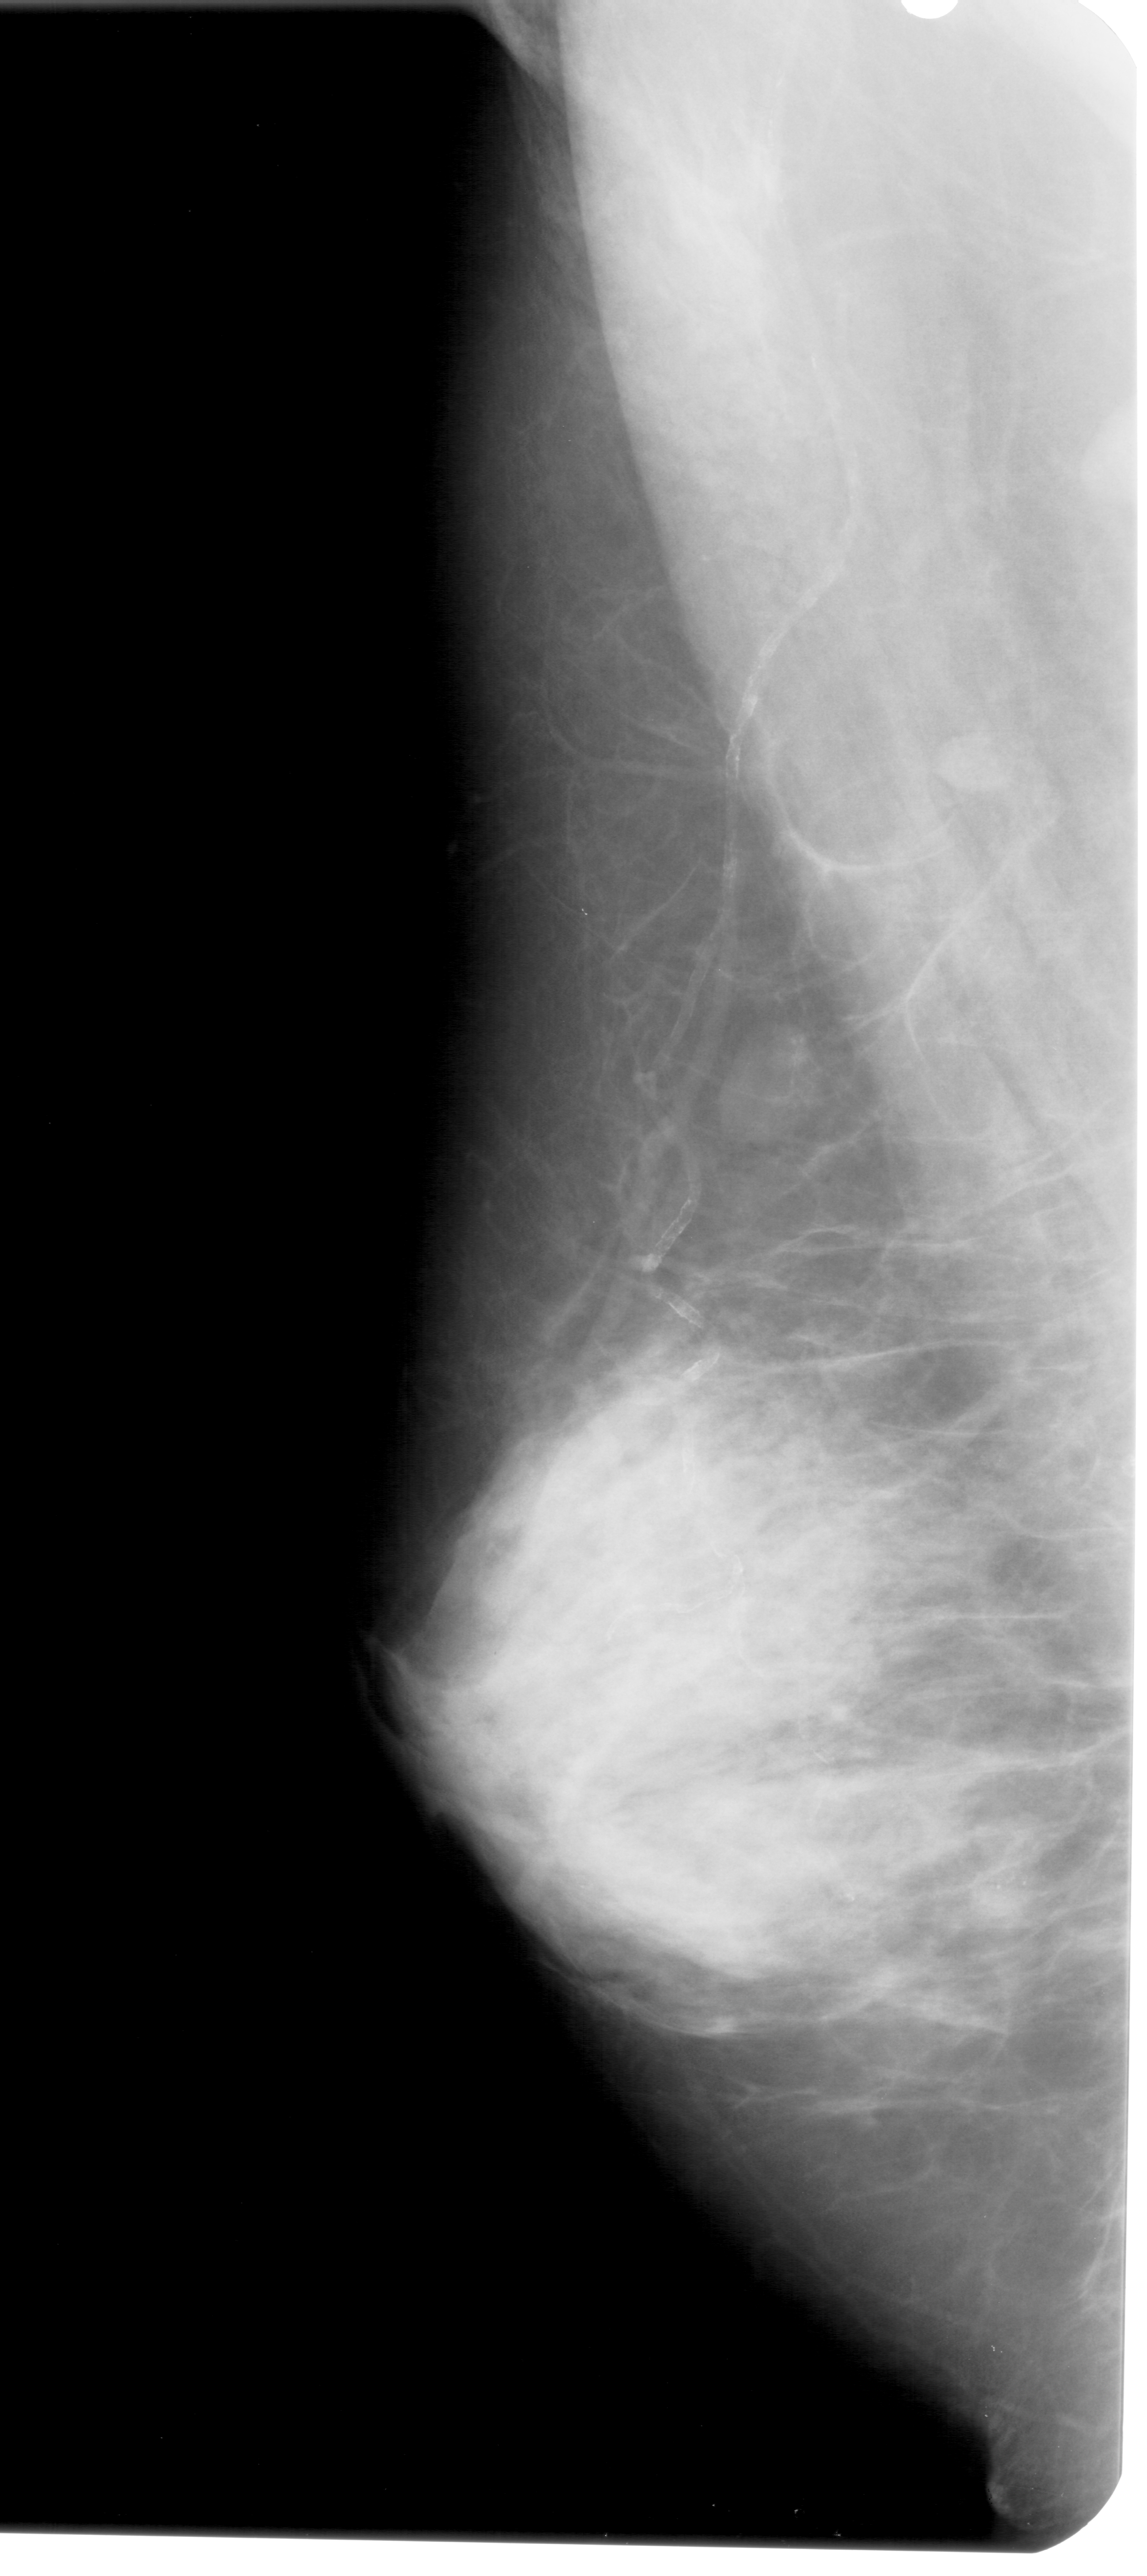
Scanned film-screen mammogram, left breast, mediolateral oblique (MLO) view, breast composition: extremely dense (BI-RADS density category 4 of 4).
Finding: calcifications, morphology pleomorphic, distribution clustered; BI-RADS assessment category 4; pathology result (as recorded, not read from the image): benign.